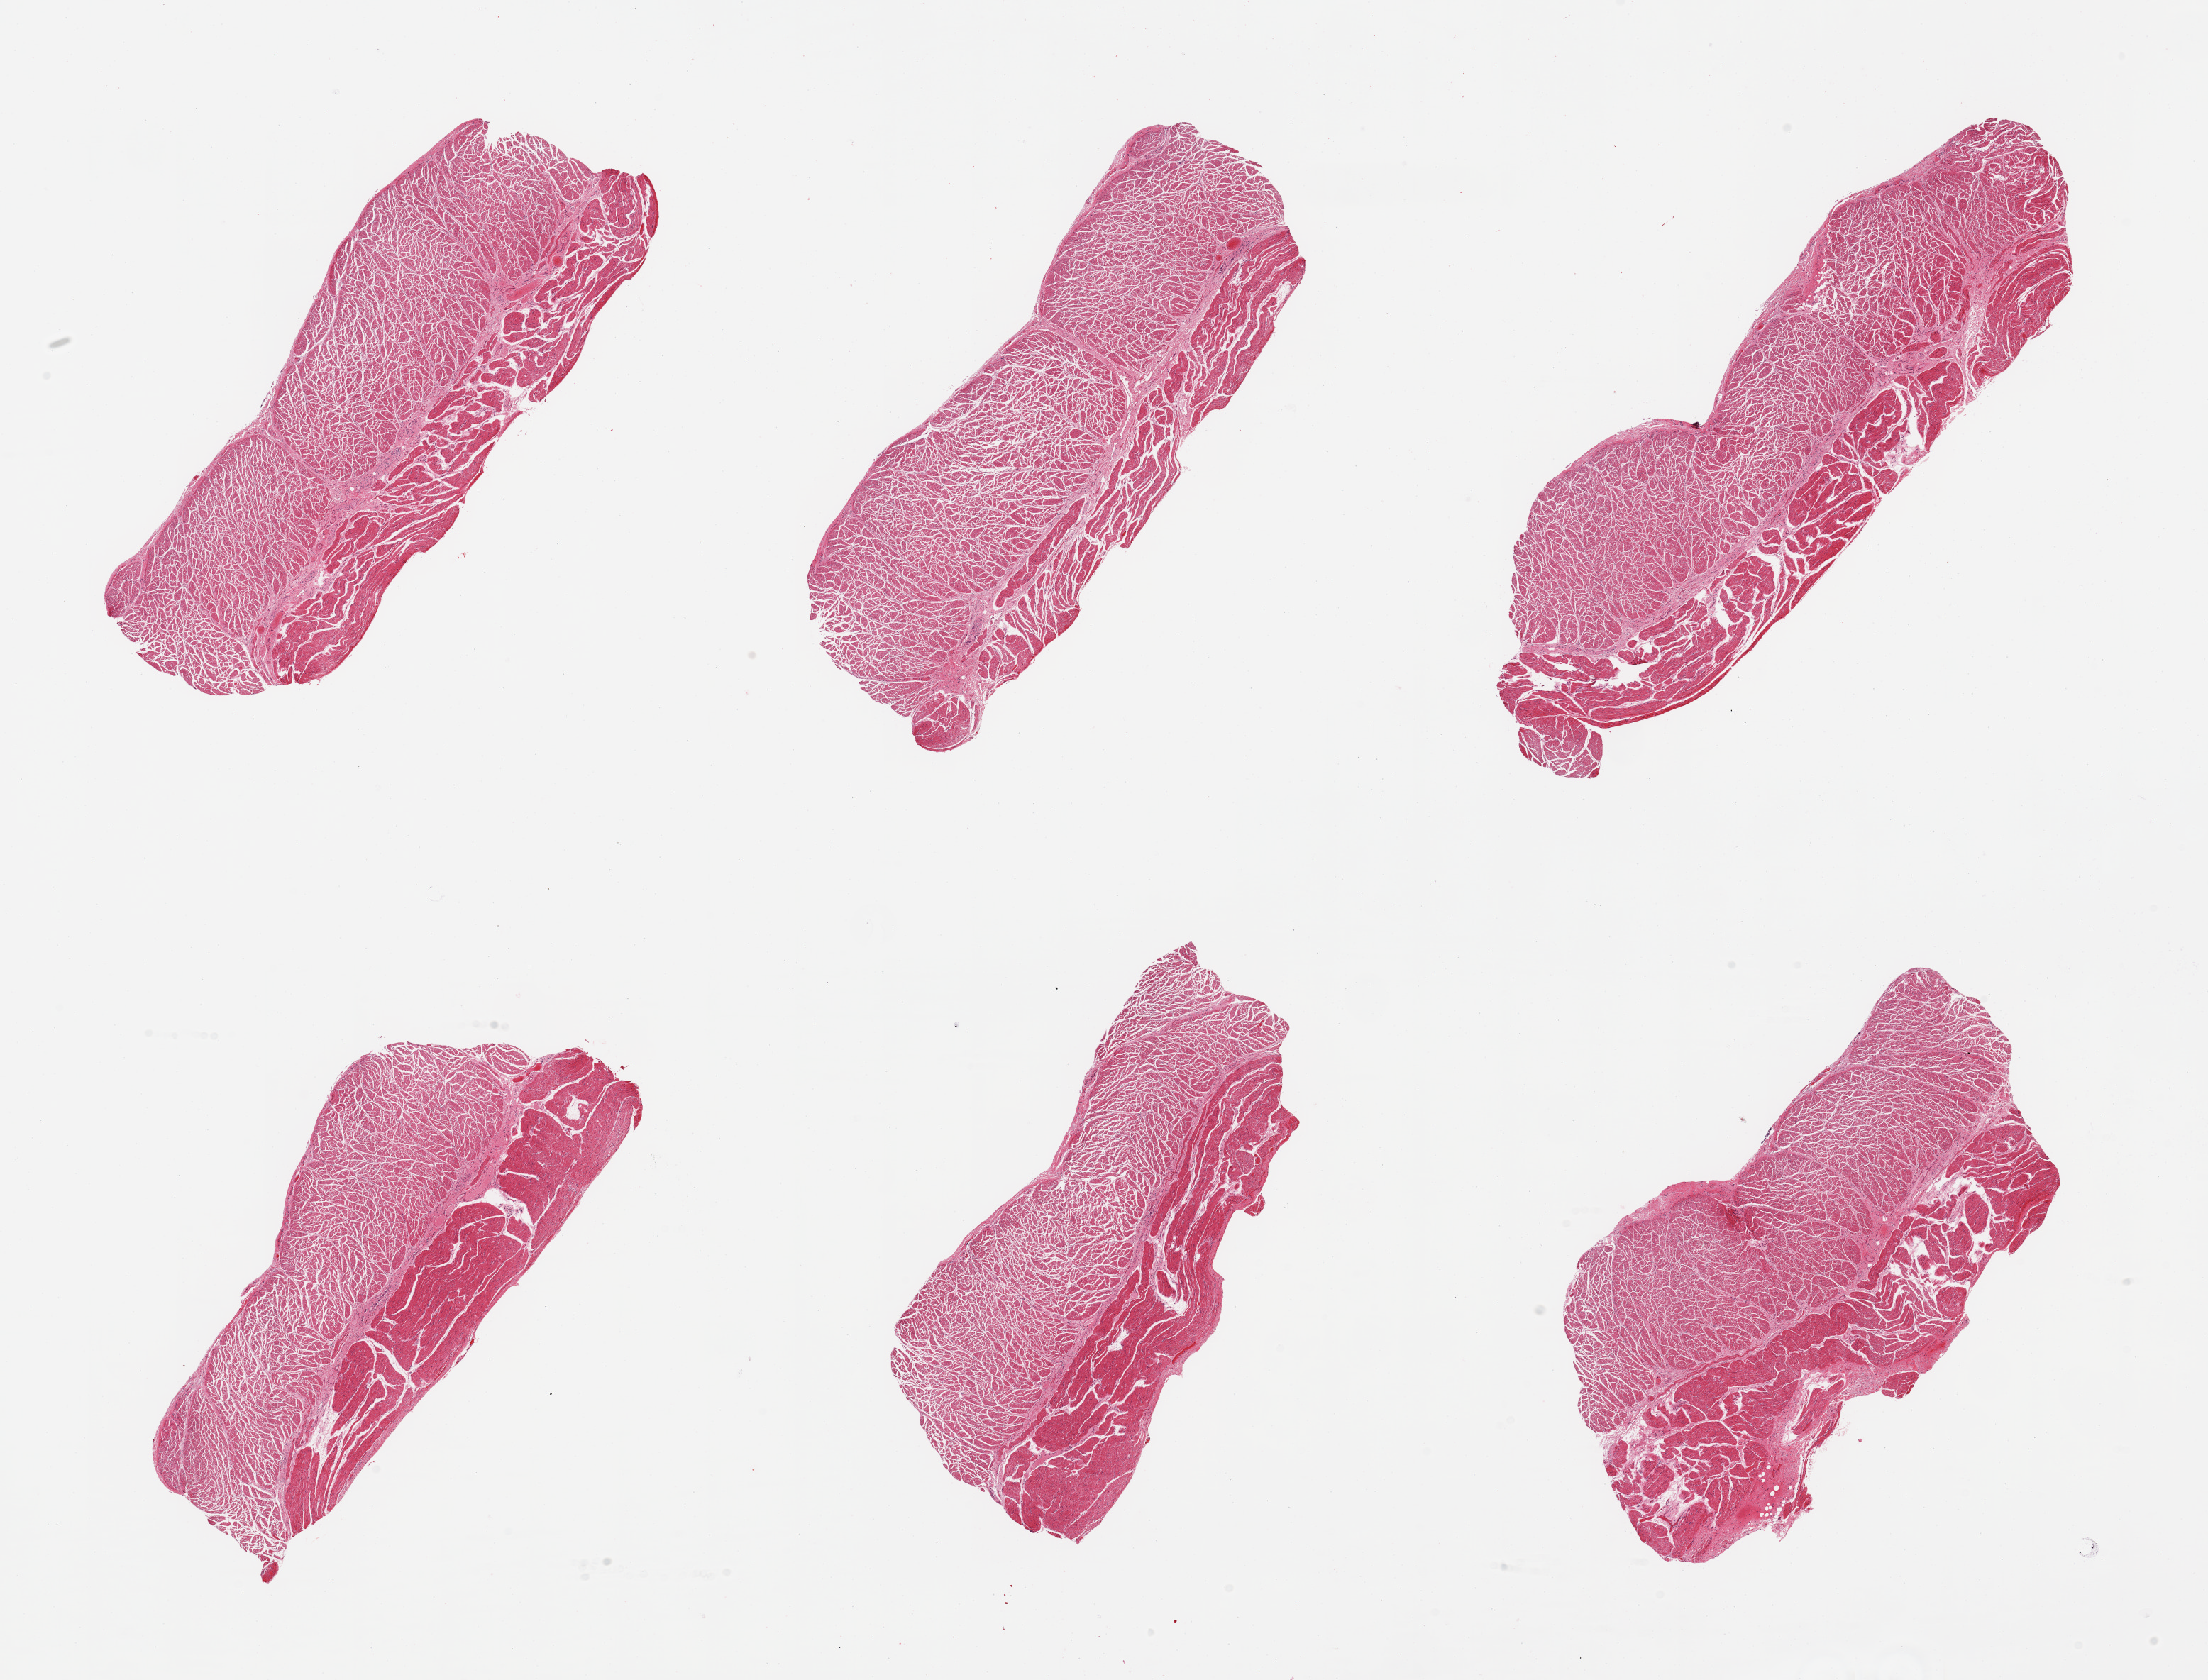
Hematoxylin and eosin (H&E) whole-slide image, a low-resolution overview of the entire scanned area, about 24.6 x 18.7 mm (slide scanned at 20x), PAXgene-fixed, paraffin-embedded tissue, sampled site (target tissue): esophageal muscle, donor tissue sample. Donor: male.
• pathologist's review note for this sample: 6 pieces; well trimmed